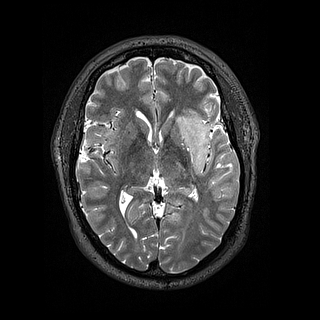
Brain MRI from a brain-tumour surgery series, one axial slice; slice 85 of 144 in the series (ordered by position); 1.2 mm slice thickness; 320 × 320 image matrix, field of view 254 × 254 mm. Case-level facts recorded for this patient, not image findings: histopathology: Astrocytoma; WHO grade: 2; IDH mutation: yes; tumour location: Left Insular.
Outlined on this slice (expert manual segmentation):
- tumour: bounding box (x1, y1, x2, y2) in pixels: (177, 108, 211, 175)